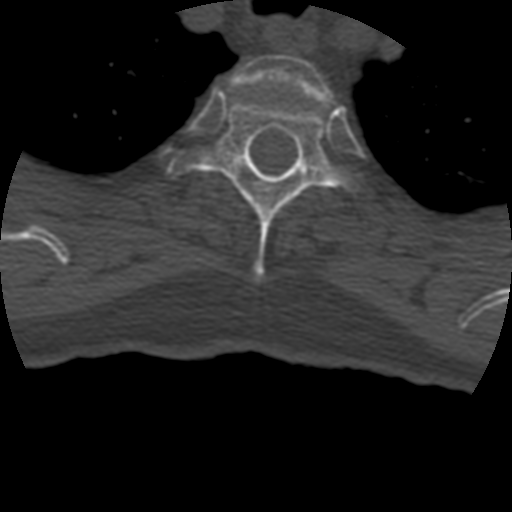
CT including the spine, one axial slice. Position 355 of 399 along the scan axis. Reconstruction kernel STANDARD. 120 kVp. Bone window (W 1800 / L 400 HU). 512 × 512 image matrix, field of view 160 × 160 mm. Patient age 69 years. Case-level facts recorded for this patient, not image findings: primary cancer: prostate.
Outlined on this slice (semi-automatically segmented with operator editing):
- T2 vertebra: box from (x=231, y=55) to (x=334, y=103) px
- T3 vertebra: (x=169, y=94)–(x=364, y=280)